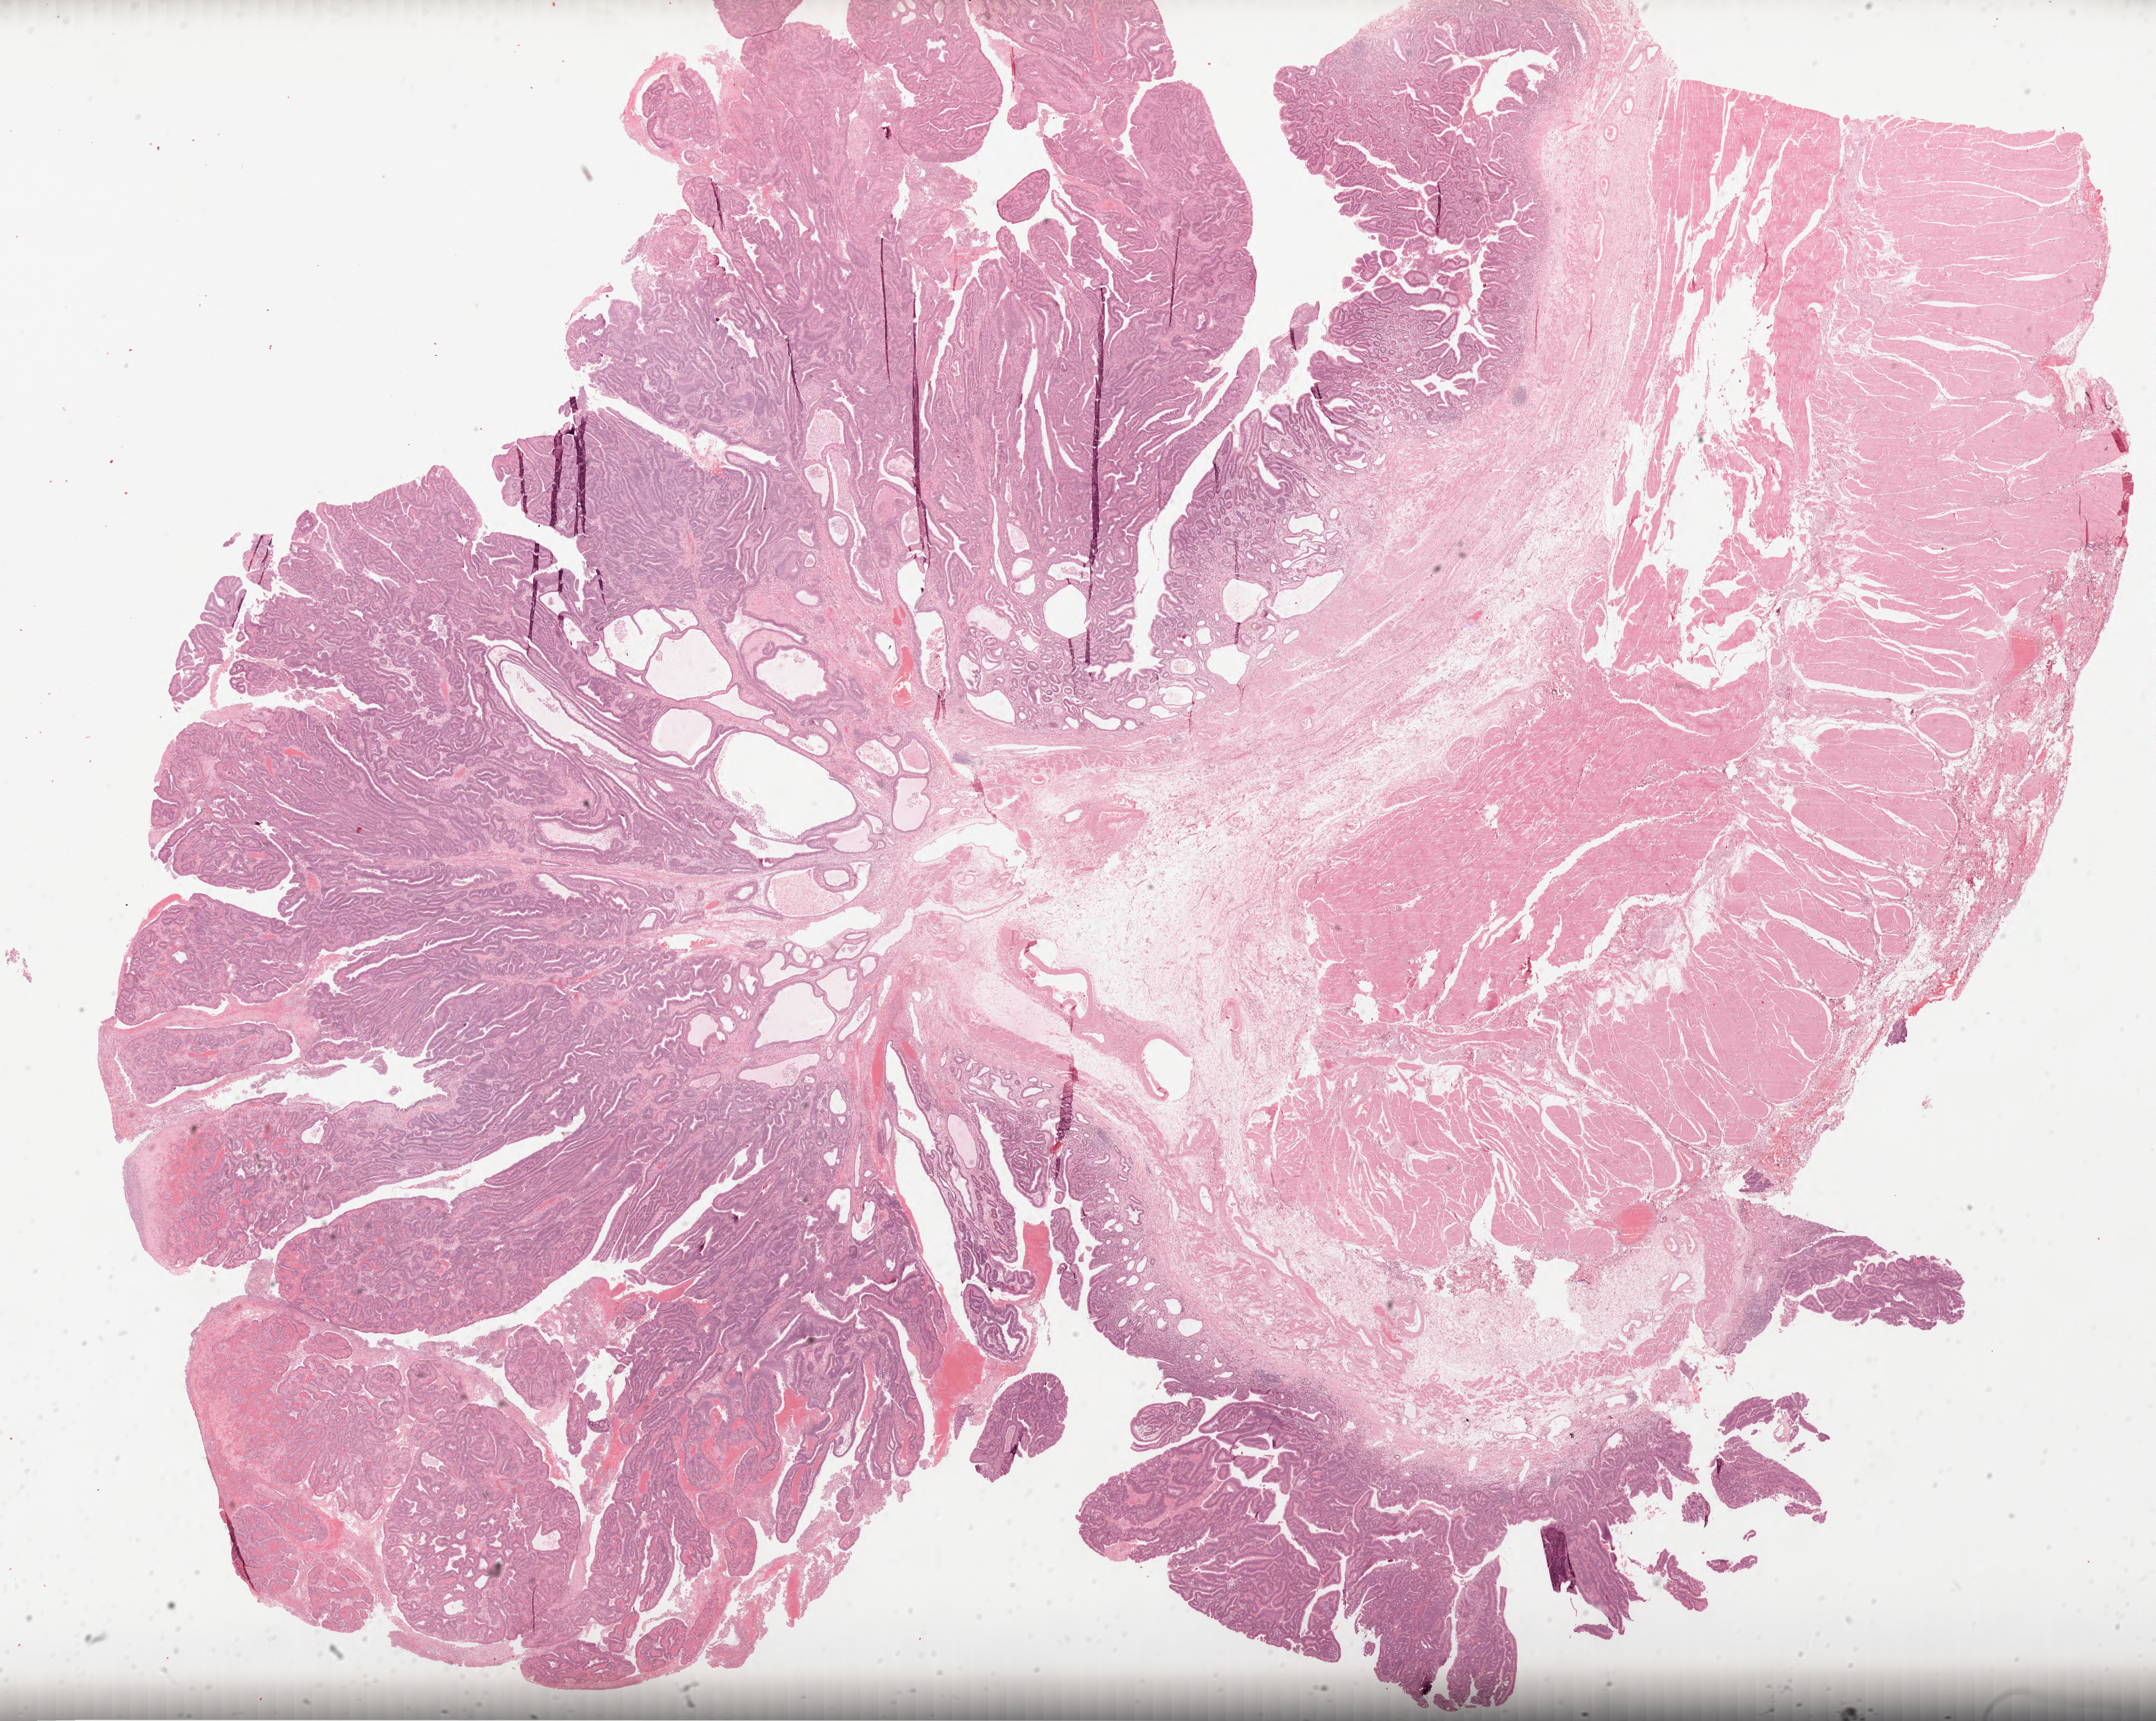
Digitized H&E-stained tissue section (whole slide), low-resolution overview of the scanned area, about 28.3 x 22.6 mm (from a 40x scan), formalin-fixed paraffin-embedded (FFPE) diagnostic section, esophagus, primary tumour sample. Patient: male, age at initial diagnosis 77 years.
Diagnosis: Adenocarcinoma, NOS (lower third of esophagus).